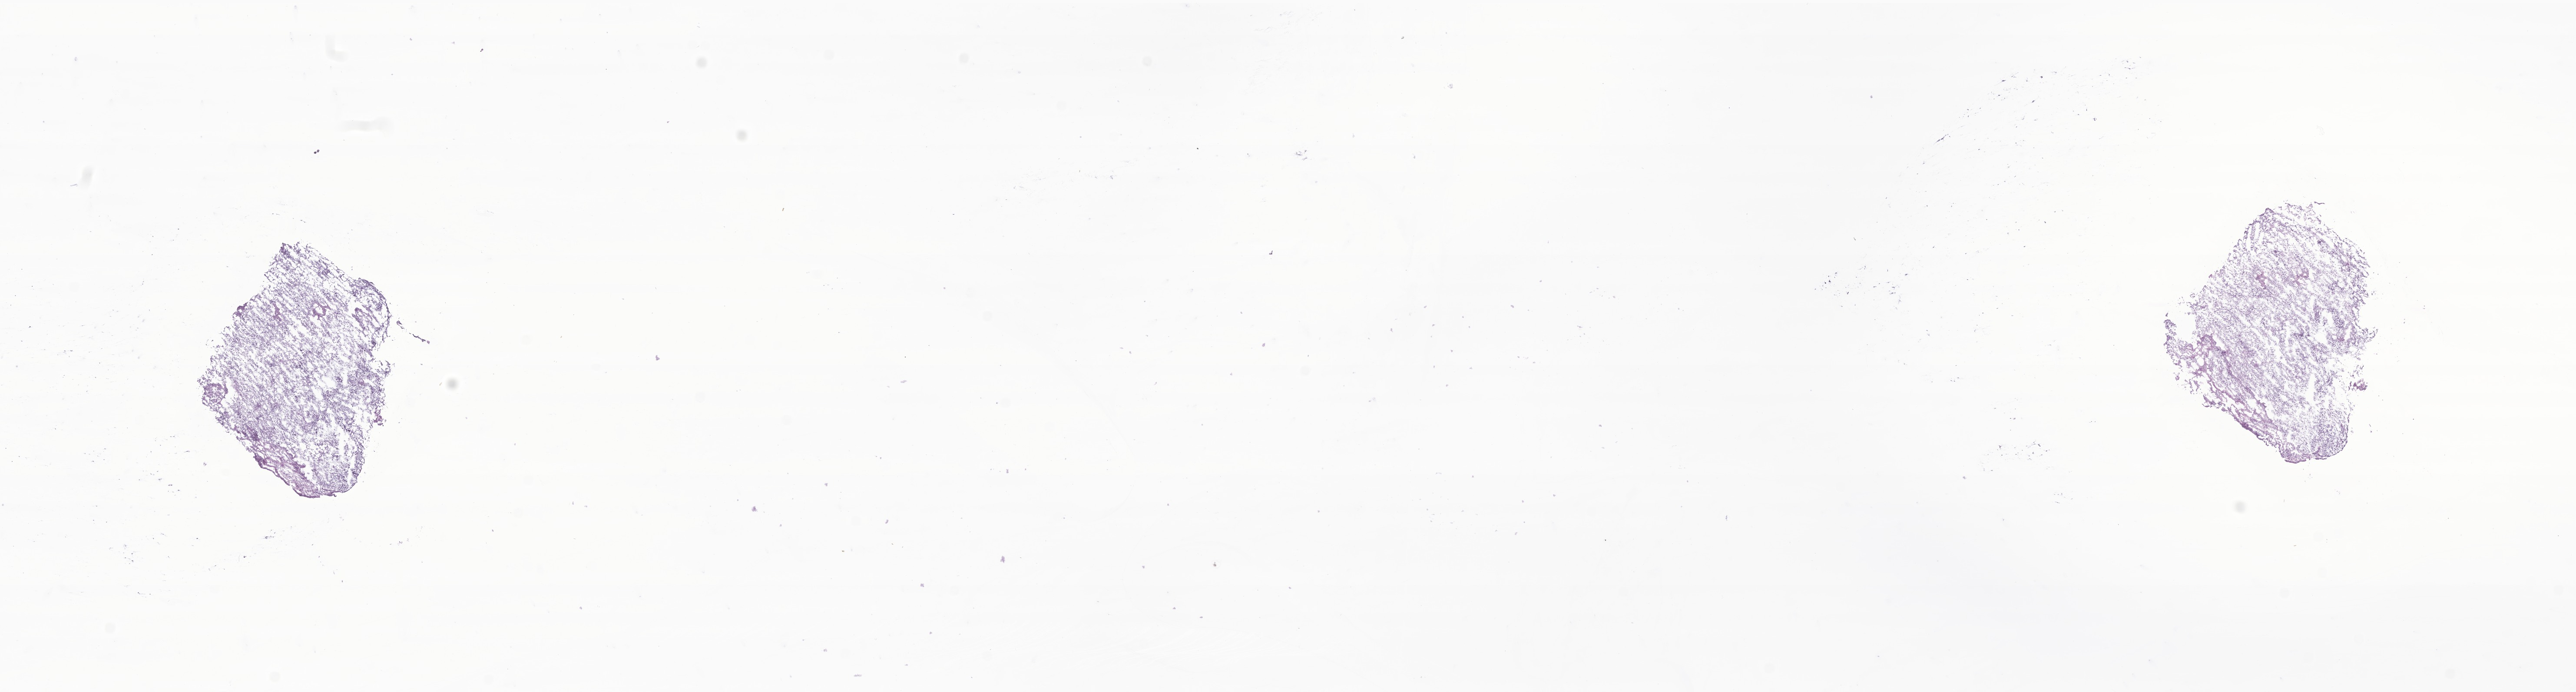
H&E whole-slide image of tumor tissue from the brain, a low-resolution overview of the entire scanned area, about 25.0 x 6.7 mm, frozen section. Patient: female, age 148 days.
Diagnosis (ICD-O-3 morphology term): Pilocytic astrocytoma.